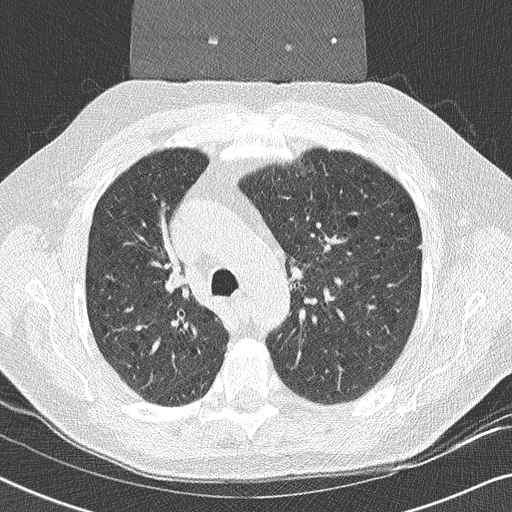
Low-dose screening chest CT, one axial slice; position 168 of 252 along the scan axis; reconstruction kernel B50f; 120 kVp; lung window (W 1500 / L -600 HU); 2 mm slice thickness; 512 × 512 image matrix, field of view 330 × 330 mm.
Structures marked on this image (manually delineated by an expert):
- lesion 1 (tumor, upper lobe of right lung): bounding box <166,270,186,292> (left, top, right, bottom; pixels)